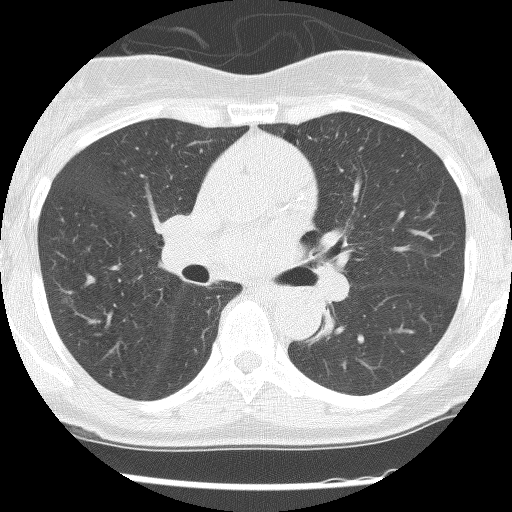
Axial slice from a low-dose chest CT screening exam. Second annual screen. Lung window (W 1500 / L -600 HU). 2.5 mm slice thickness. Lung (sharp) reconstruction kernel (BONE). Slice 53 of 120 in the series. 512 × 512 image matrix. Female, age 62 years at enrolment. Former smoker at enrolment.
Lesion marked by an expert reader, bounding box <299,298,352,348> (left, top, right, bottom; pixels). Reader record for this screening exam (exam-level; its link to the box is not recorded): non-calcified nodule or mass ≥4 mm, right upper lobe, 30 × 30 mm, poorly defined margins, ground glass attenuation, pre-existing on the prior screen: yes; interval growth: no. Note: the box lies in the patient's left hemithorax on this image, whereas the reader's record names the right lung; they may be different findings.